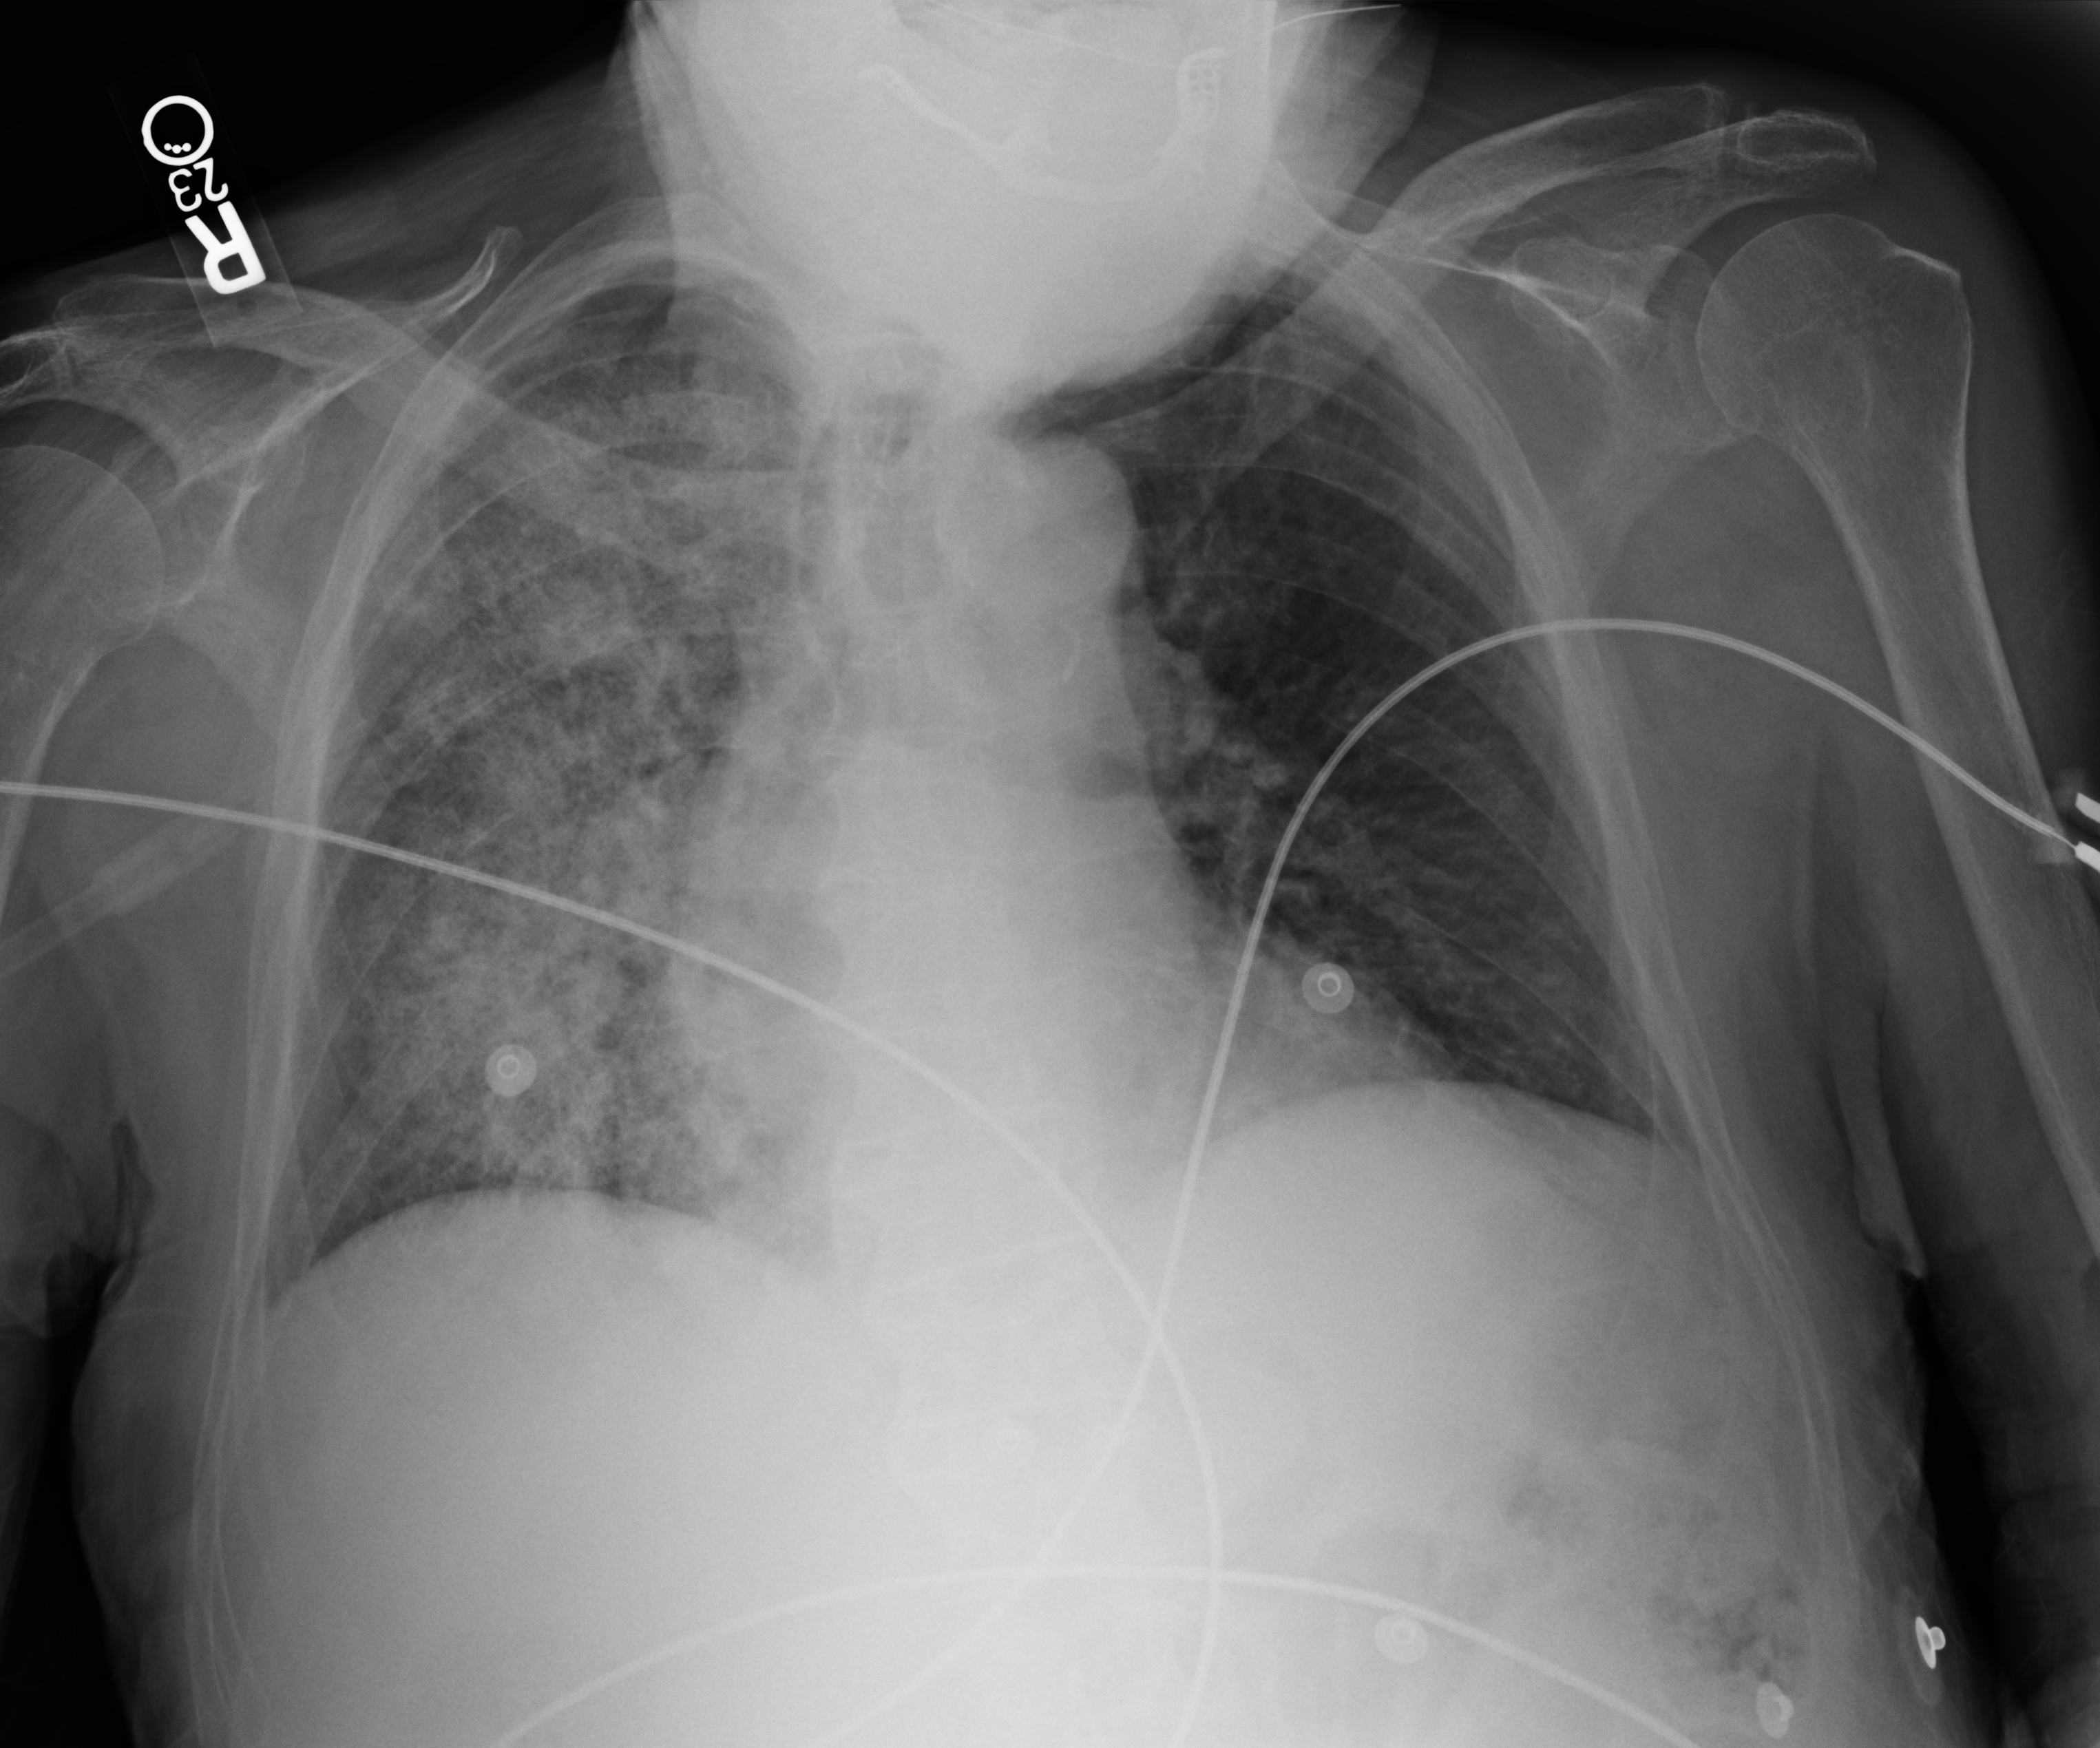
Chest X-ray (portable); anteroposterior (AP) projection. Patient hospitalised with COVID-19; male, aged 75–90 years.
Hospital-stay facts (about this admission, not read from this image; timing relative to this image not recorded):
- admitted to intensive care during this hospital stay: no
- mechanically ventilated during this hospital stay: no